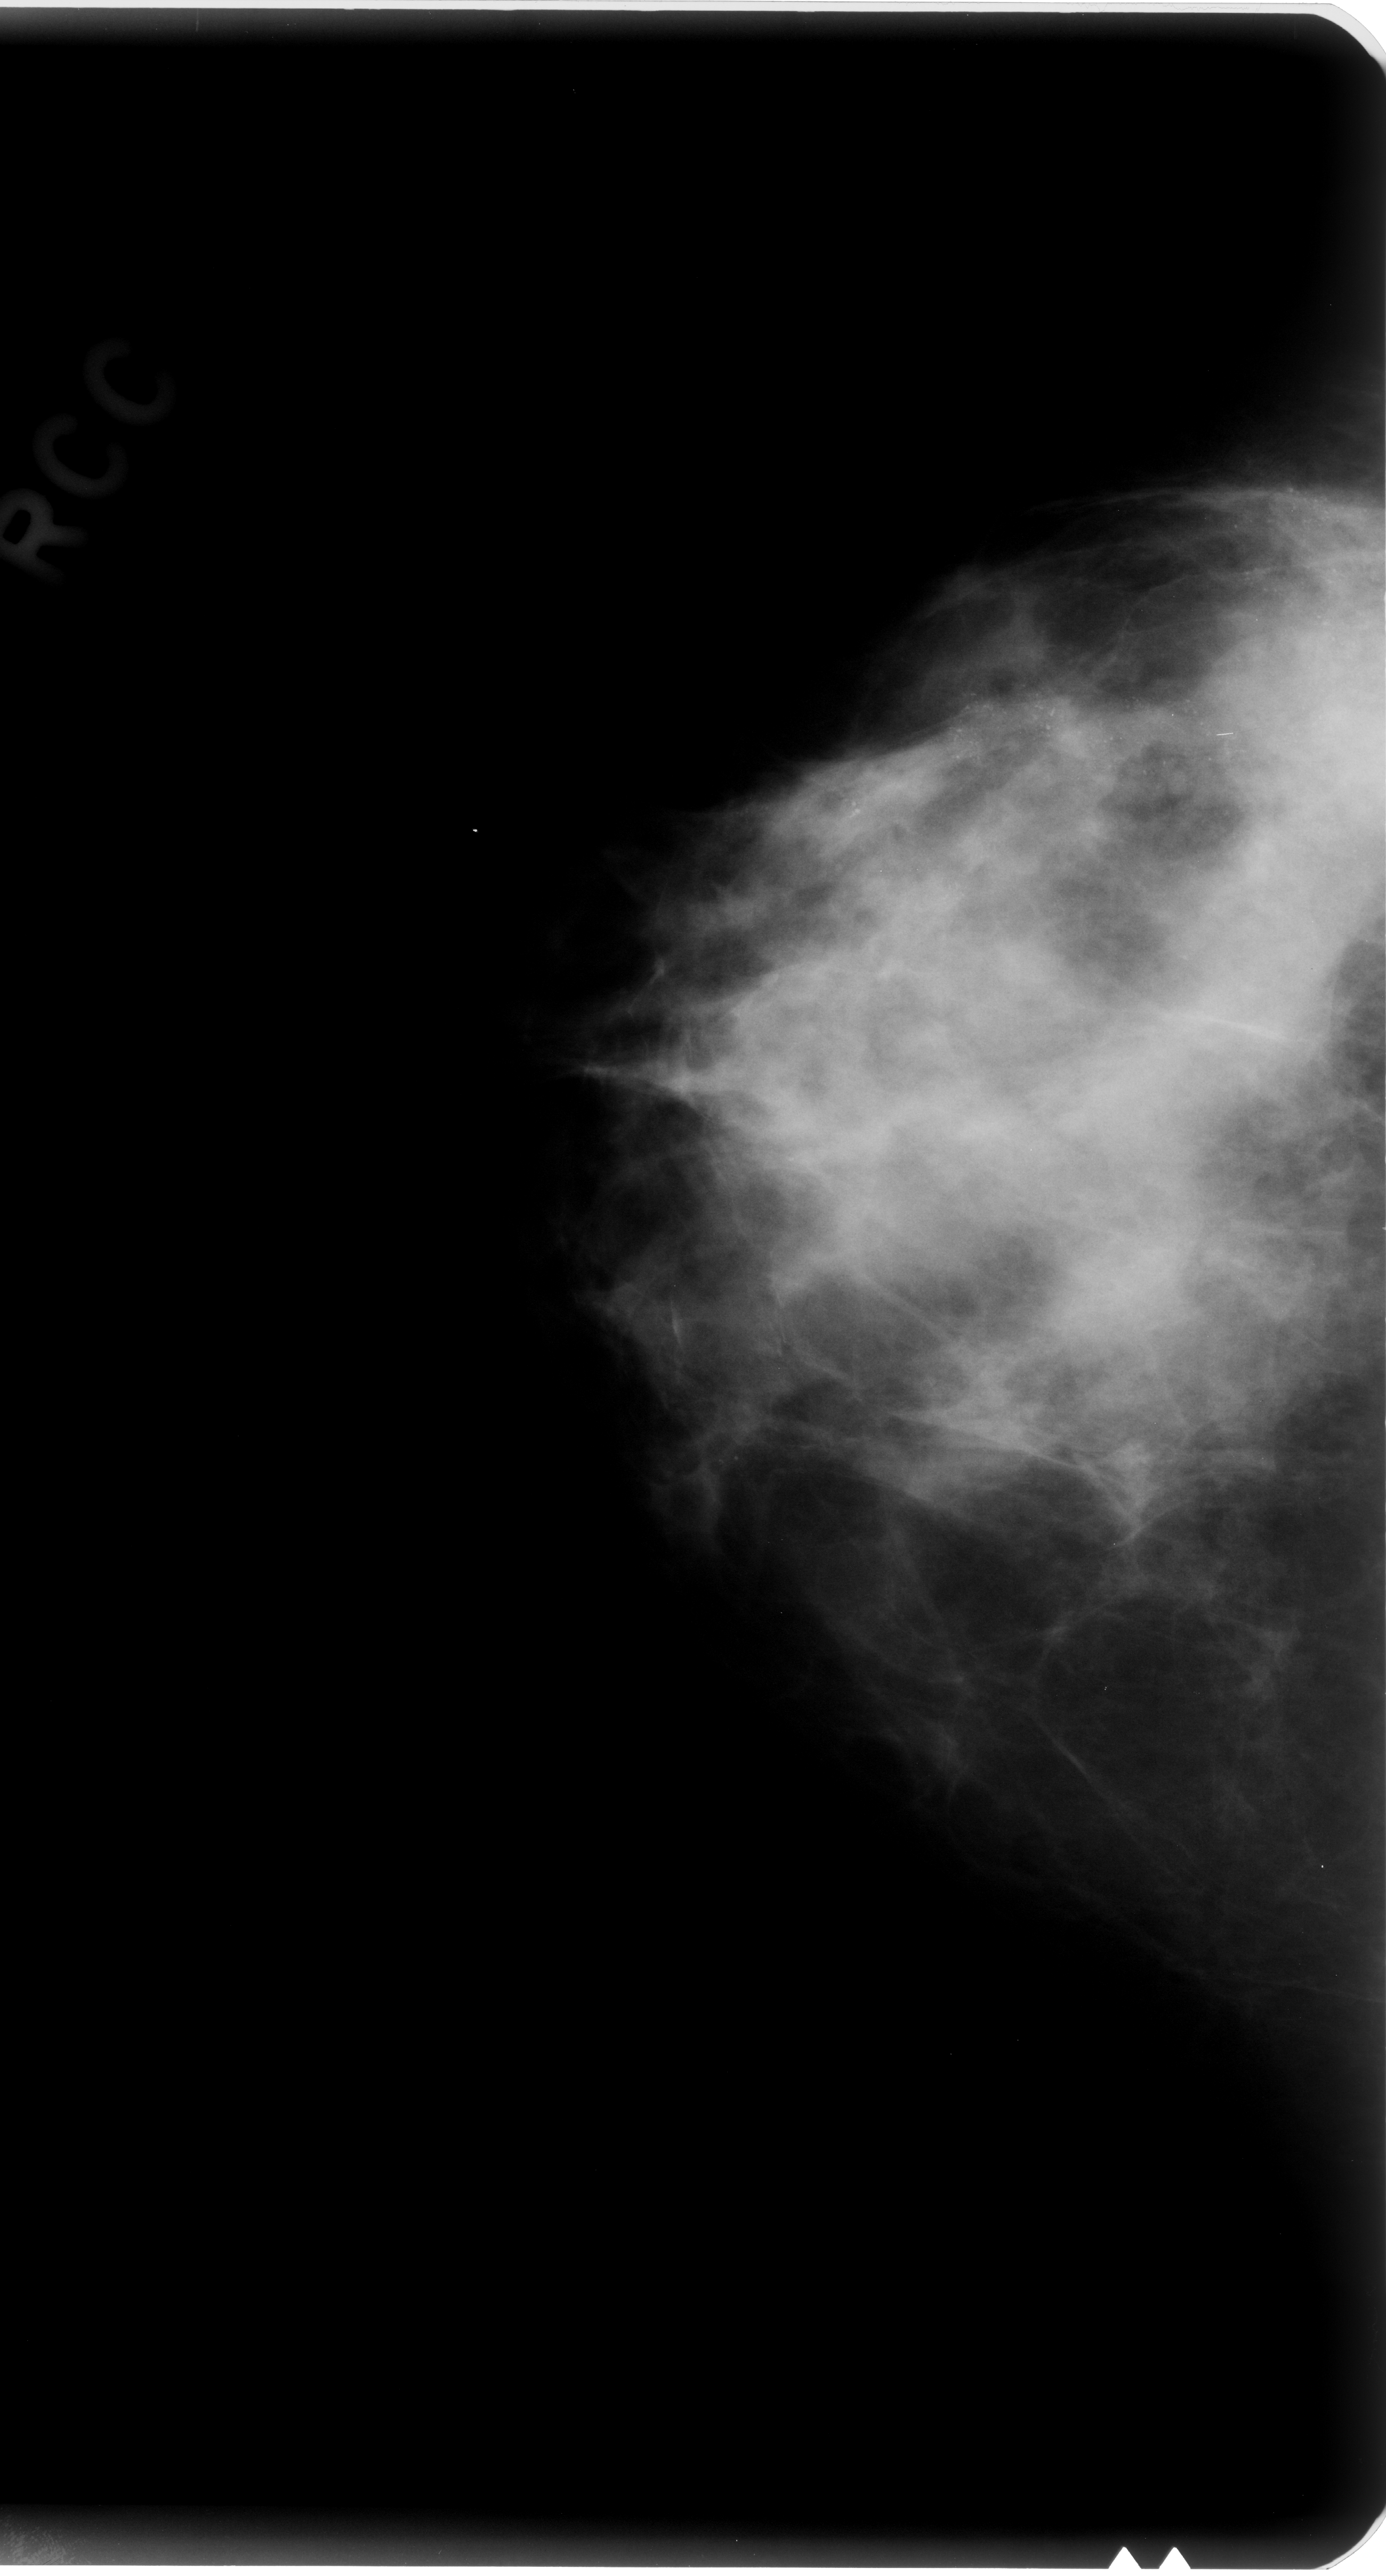
Digitized screen-film mammogram; right breast; CC view.
Marked abnormality: calcifications, morphology pleomorphic, distribution regional; BI-RADS assessment category 5; pathology (as recorded): malignant.